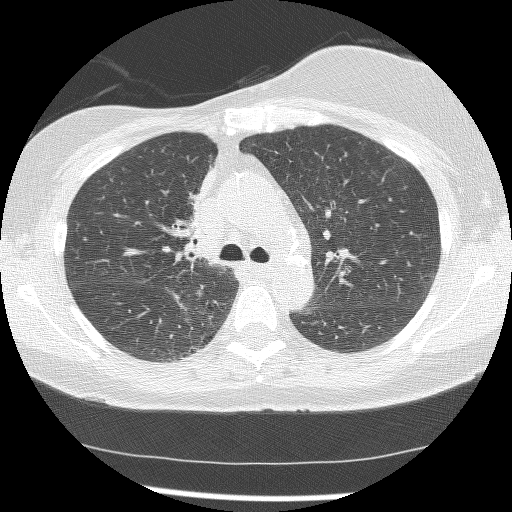
Chest CT (low-dose screening protocol), one axial image. Baseline annual screen. Lung window (W 1500 / L -600 HU). Lung (sharp) reconstruction kernel (BONE). 120 kVp. Female, age 56 years at enrolment. Current smoker at enrolment.
Expert-annotated lung lesion, bounding box <163,165,219,263> (left, top, right, bottom; pixels). The screening reader recorded 2 non-calcified nodules or masses ≥4 mm on this exam (right lower lobe, right middle lobe); which of them this box marks is not recorded. Official screen result: positive, change unspecified: nodule(s) >= 4 mm or enlarging nodule(s), mass(es), or other non-specific abnormalities suspicious for lung cancer.